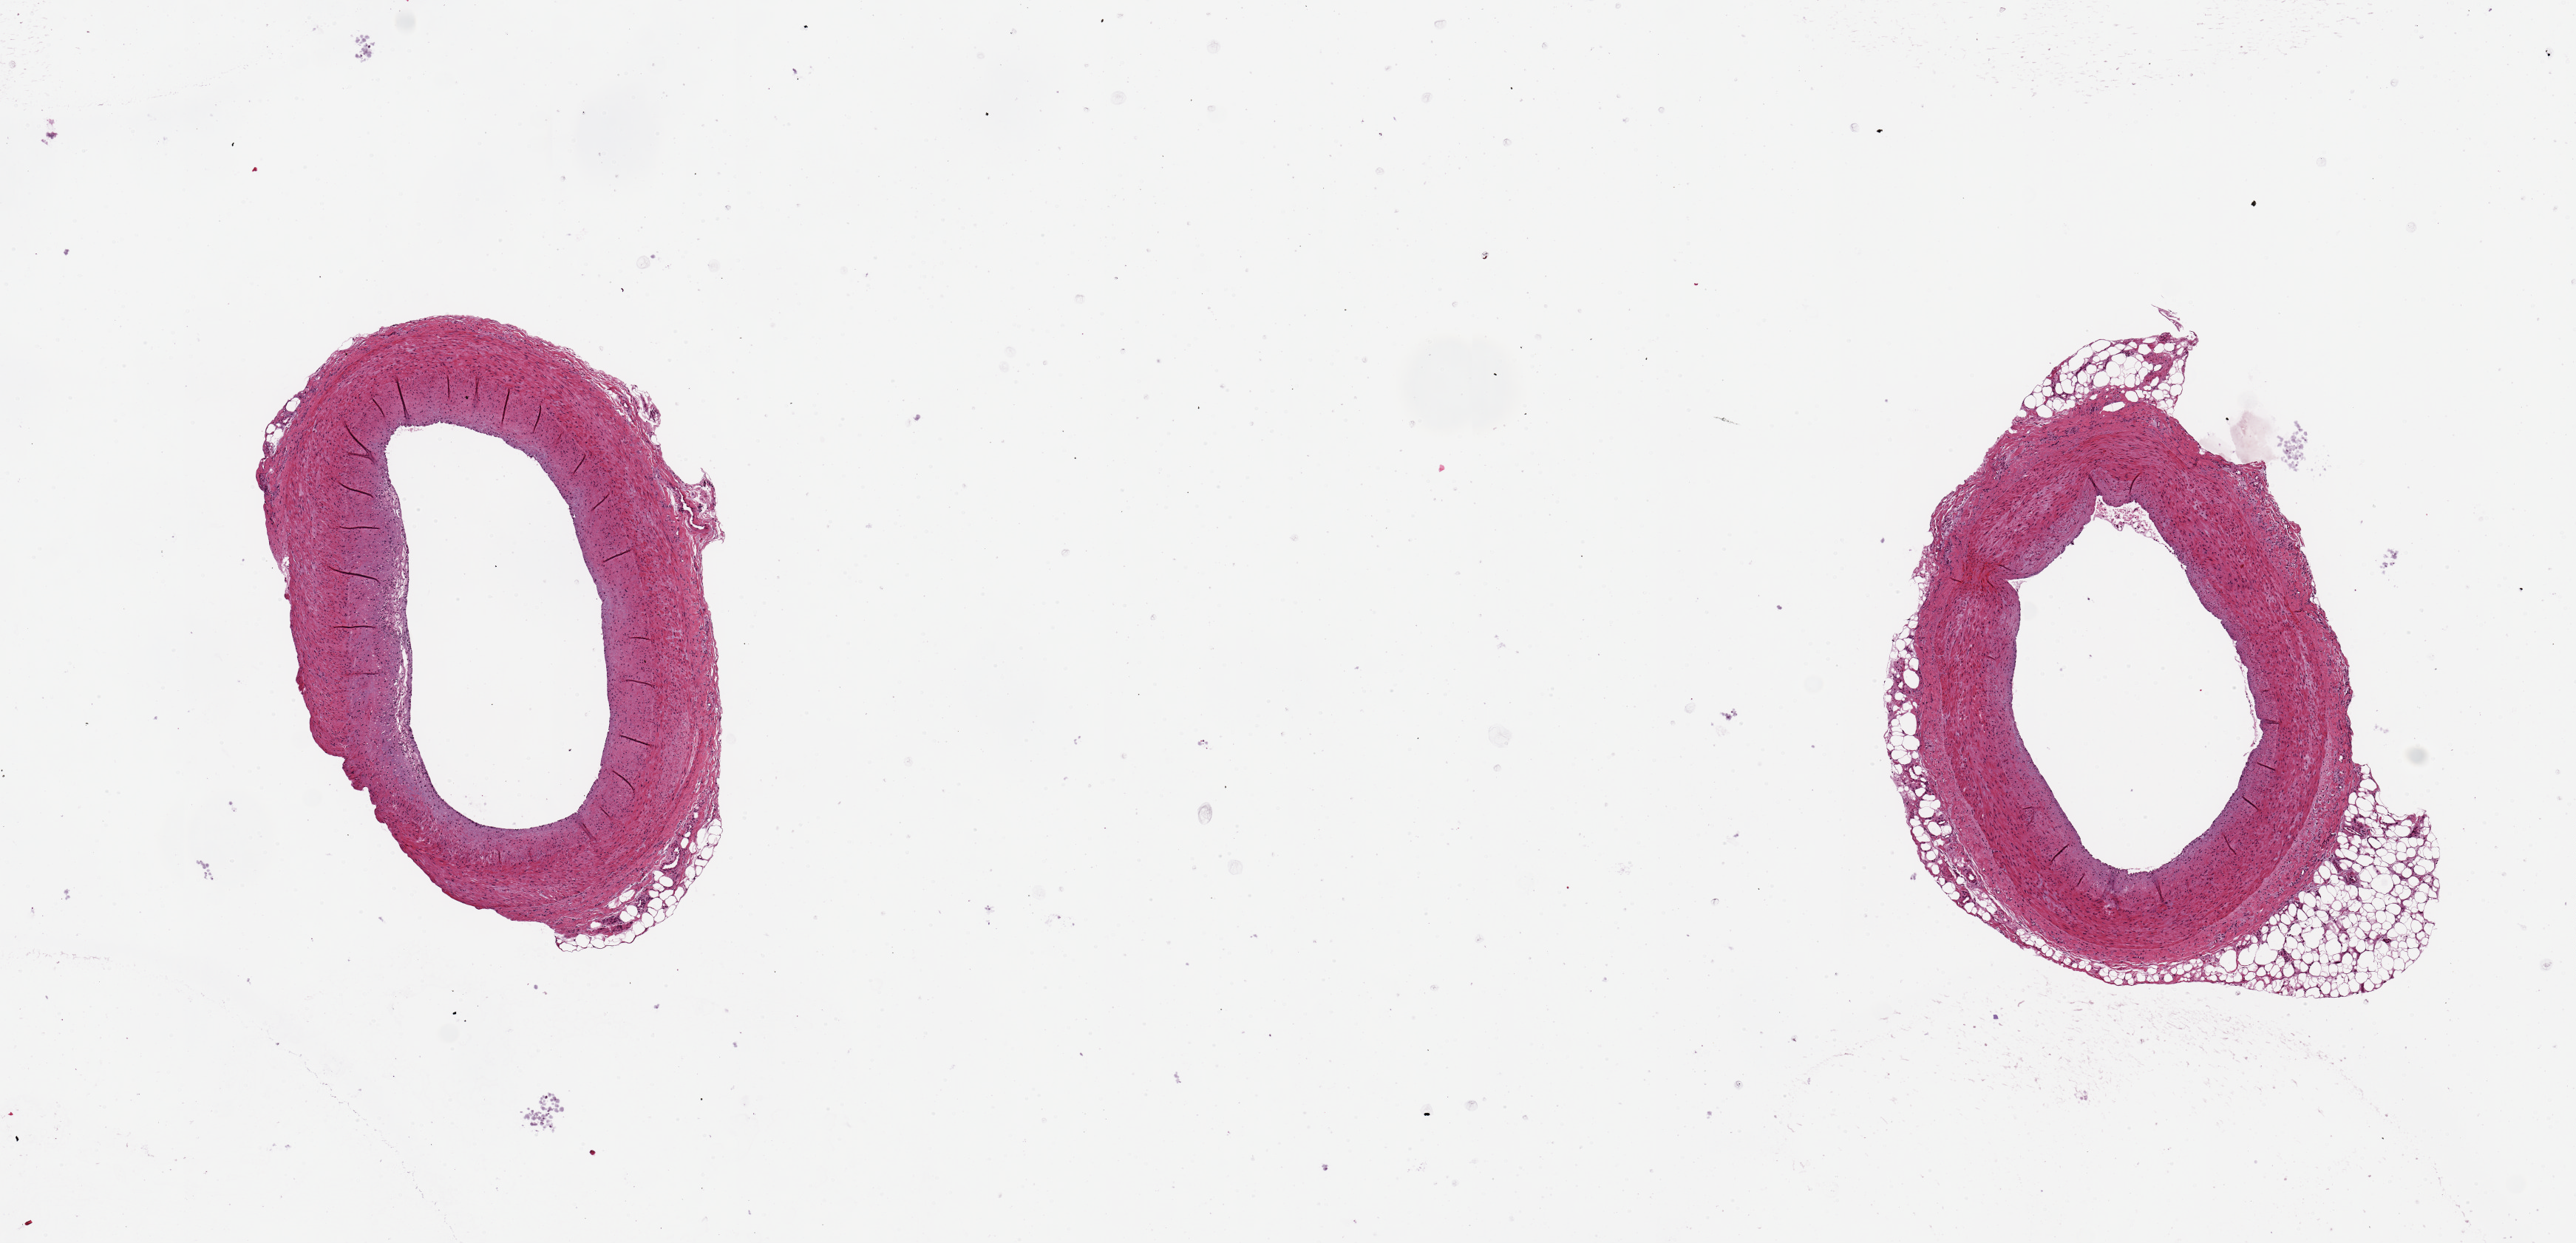
Haematoxylin and eosin whole-slide image — a low-resolution overview of the entire scanned area, about 13.8 x 6.7 mm, PAXgene-fixed, paraffin-embedded tissue, target tissue: coronary artery, tissue donor sample. Donor sex: male.
Reviewer comment on this tissue sample: 2 pieces ~3mm d; minimal atherosis; One aliquot has adherent nubbin of fat, ~1mm thick.